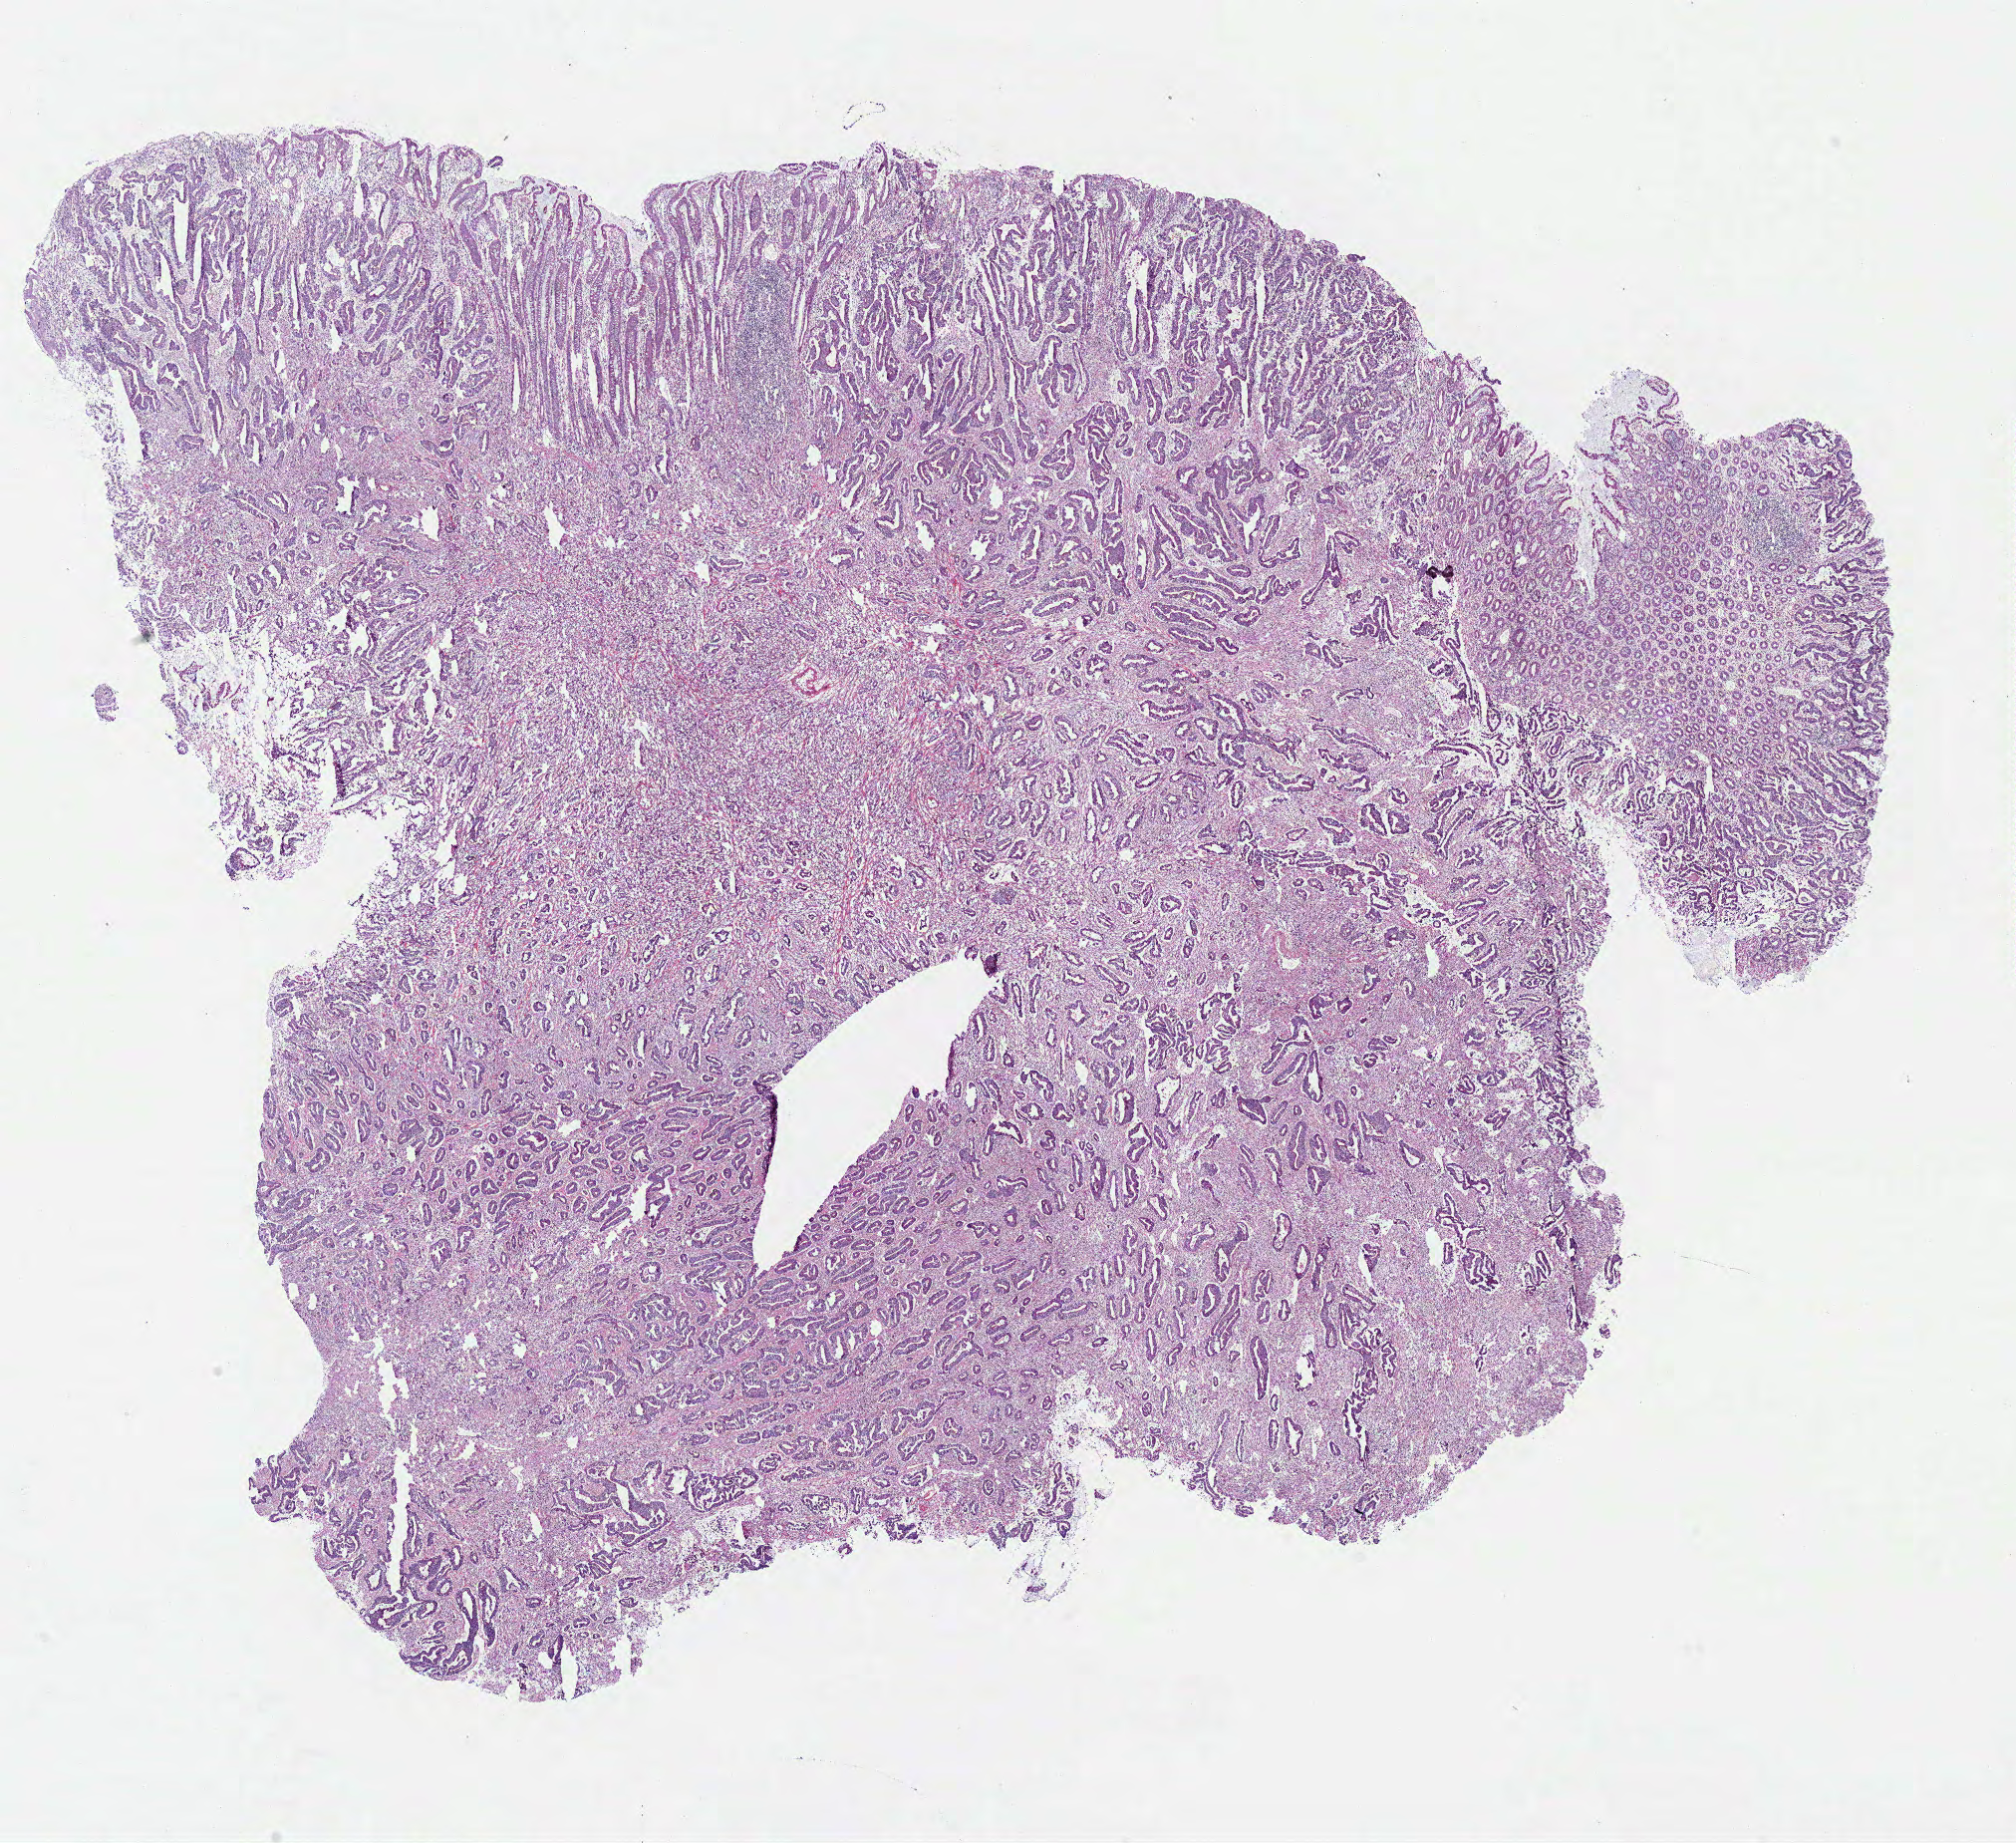
Whole-slide histology image, H&E-stained, a low-resolution overview of the entire scanned area, about 15.9 x 14.6 mm. Frozen section from the bottom of the tissue portion. Primary tumour sample from the colon. Male patient; age at initial diagnosis 44 years. Composition of this section per pathologist review: tumour cells 91%, tumour nuclei 75%, normal cells 8%, stromal cells 0%, necrosis 1%. Inflammatory infiltration, as recorded: lymphocyte infiltration 5%, monocyte infiltration 1%, neutrophil infiltration 2%.
* AJCC pathologic stage: IIA (7th edition)
* lymph nodes positive (case pathology): 0 of 44 examined
* histologic diagnosis: Adenocarcinoma, NOS (ascending colon)
* TNM: T3 N0 M0